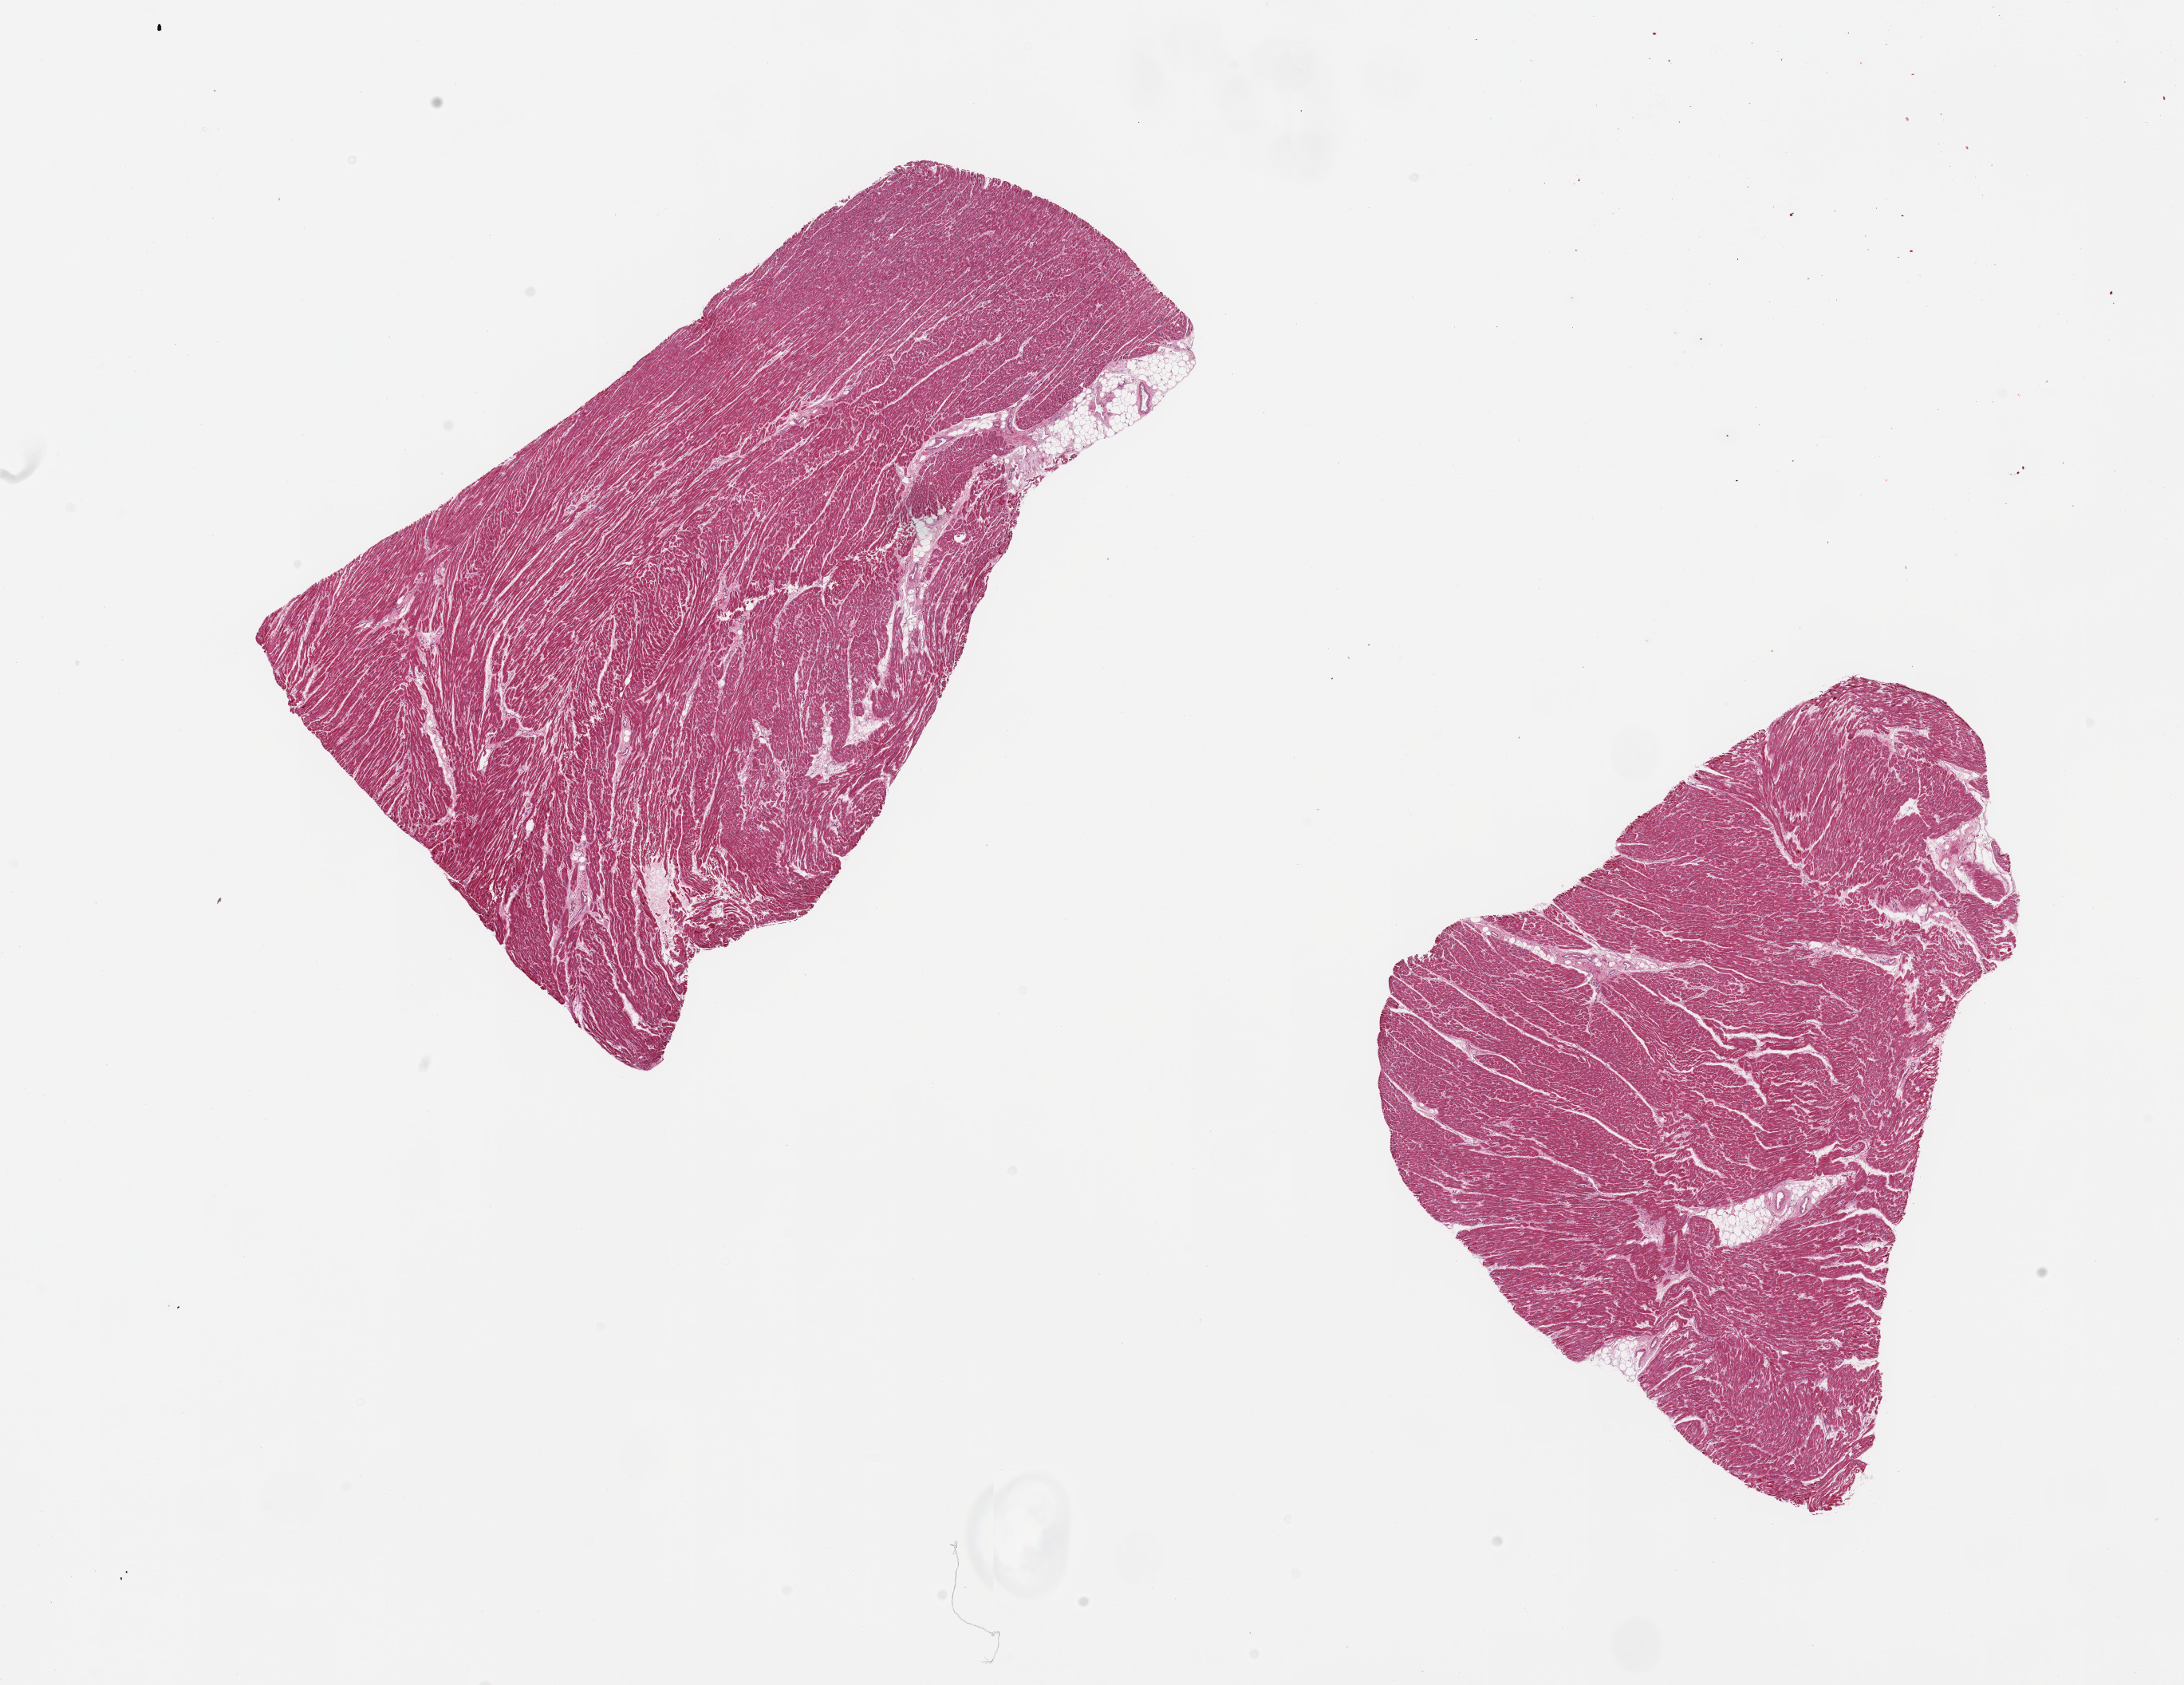
Whole-slide image, haematoxylin and eosin stain, a low-resolution overview of the entire scanned area, about 21.7 x 16.7 mm; PAXgene-fixed paraffin-embedded (PFPE) section; sampled site (target tissue): heart; donor tissue sample. Donor: female.
• pathologist's review note for this sample: 2 pieces